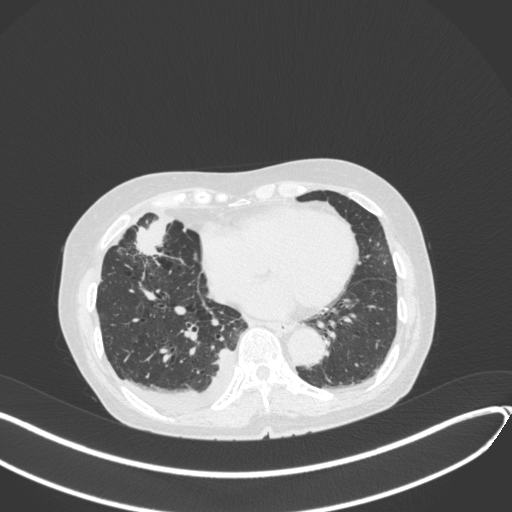
Chest CT, one axial slice; position 133 of 418 along the scan axis; 120 kVp; lung window (W 1500 / L -600 HU); 1 mm slice thickness; 512 × 512 image matrix, field of view 400 × 400 mm. Female patient, age 75 years. Case-level facts recorded for this patient, not image findings: clinical TNM (as recorded): T2a N3 M0.
Structures marked on this image (rectangle marked by the reading radiologist):
- lung tumour (recorded histology: adenocarcinoma): bounding box [x1, y1, x2, y2] px = [131, 214, 175, 264]